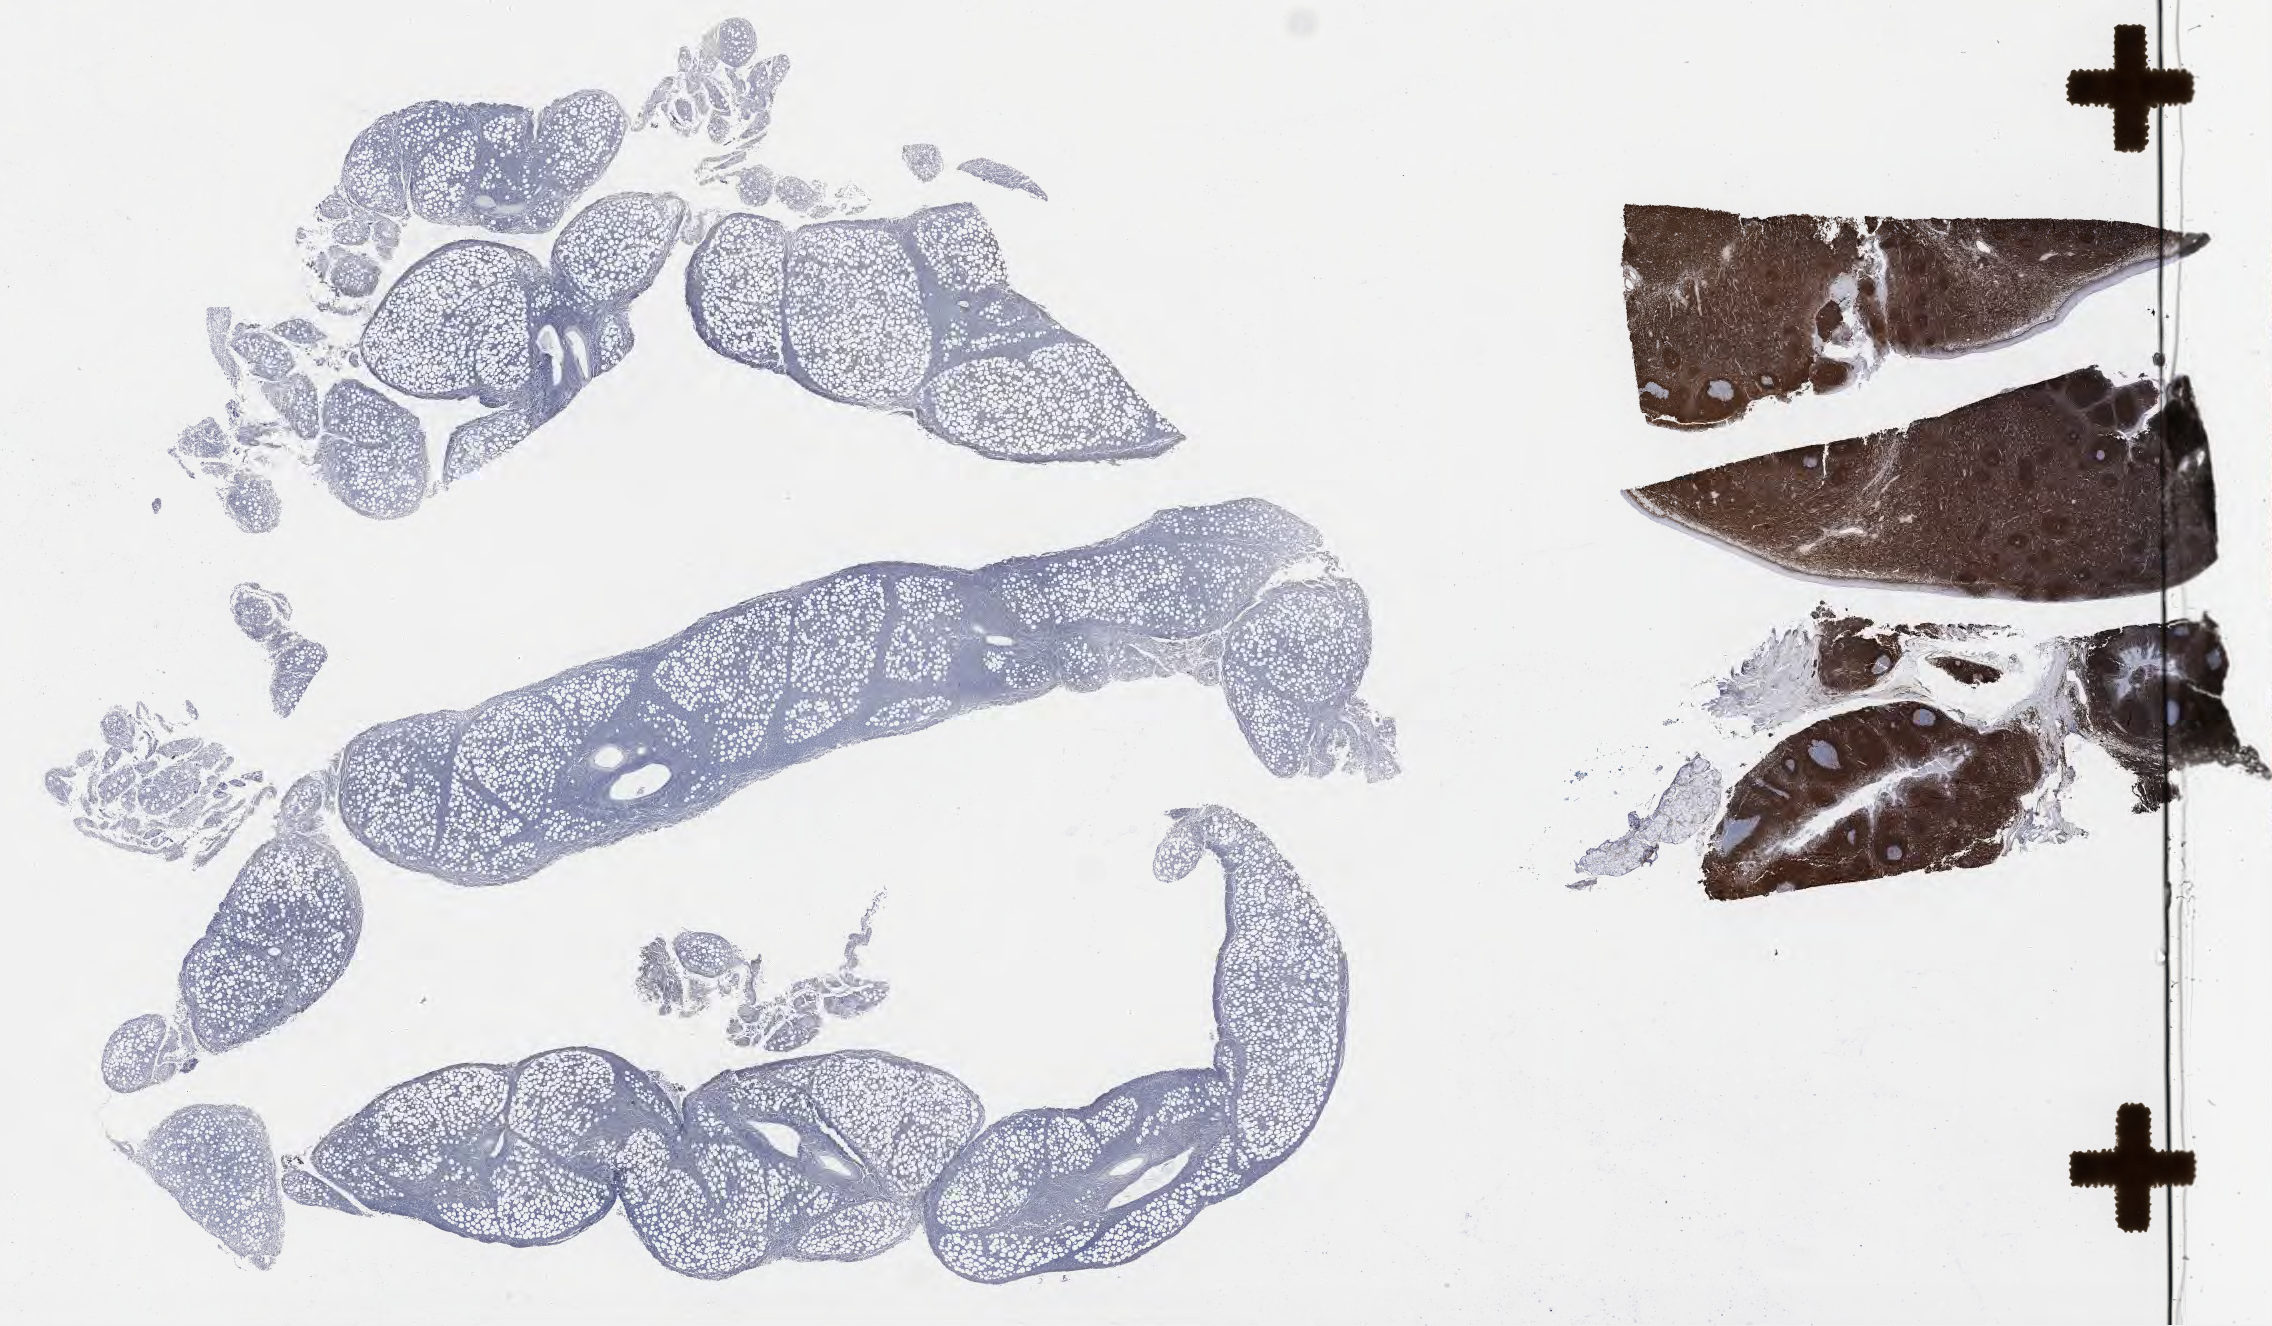
Whole-slide image, immunohistochemical stain for BCL2, whole scanned area (about 36.7 x 21.4 mm) shown as a low-resolution overview; tumor tissue; anatomic site: abdomen proper. Patient: female, age at initial diagnosis 9 years.
Histologic diagnosis: Burkitt lymphoma, NOS.